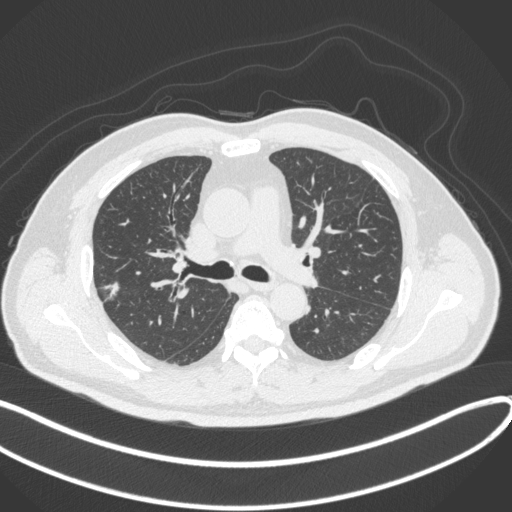
Chest CT, one axial slice. Slice 214 of 373 in the series (ordered by position). Lung window (W 1500 / L -600 HU). 1 mm slice thickness. 512 × 512 image matrix, field of view 400 × 400 mm. Male patient, age 60 years. From the clinical record (not read from this slice): clinical TNM (as recorded): T1c N0 M0.
Outlined on this slice (bounding box drawn by a radiologist):
- lung tumour (recorded histology: adenocarcinoma): bounding box <97,276,126,305> (left, top, right, bottom; pixels)